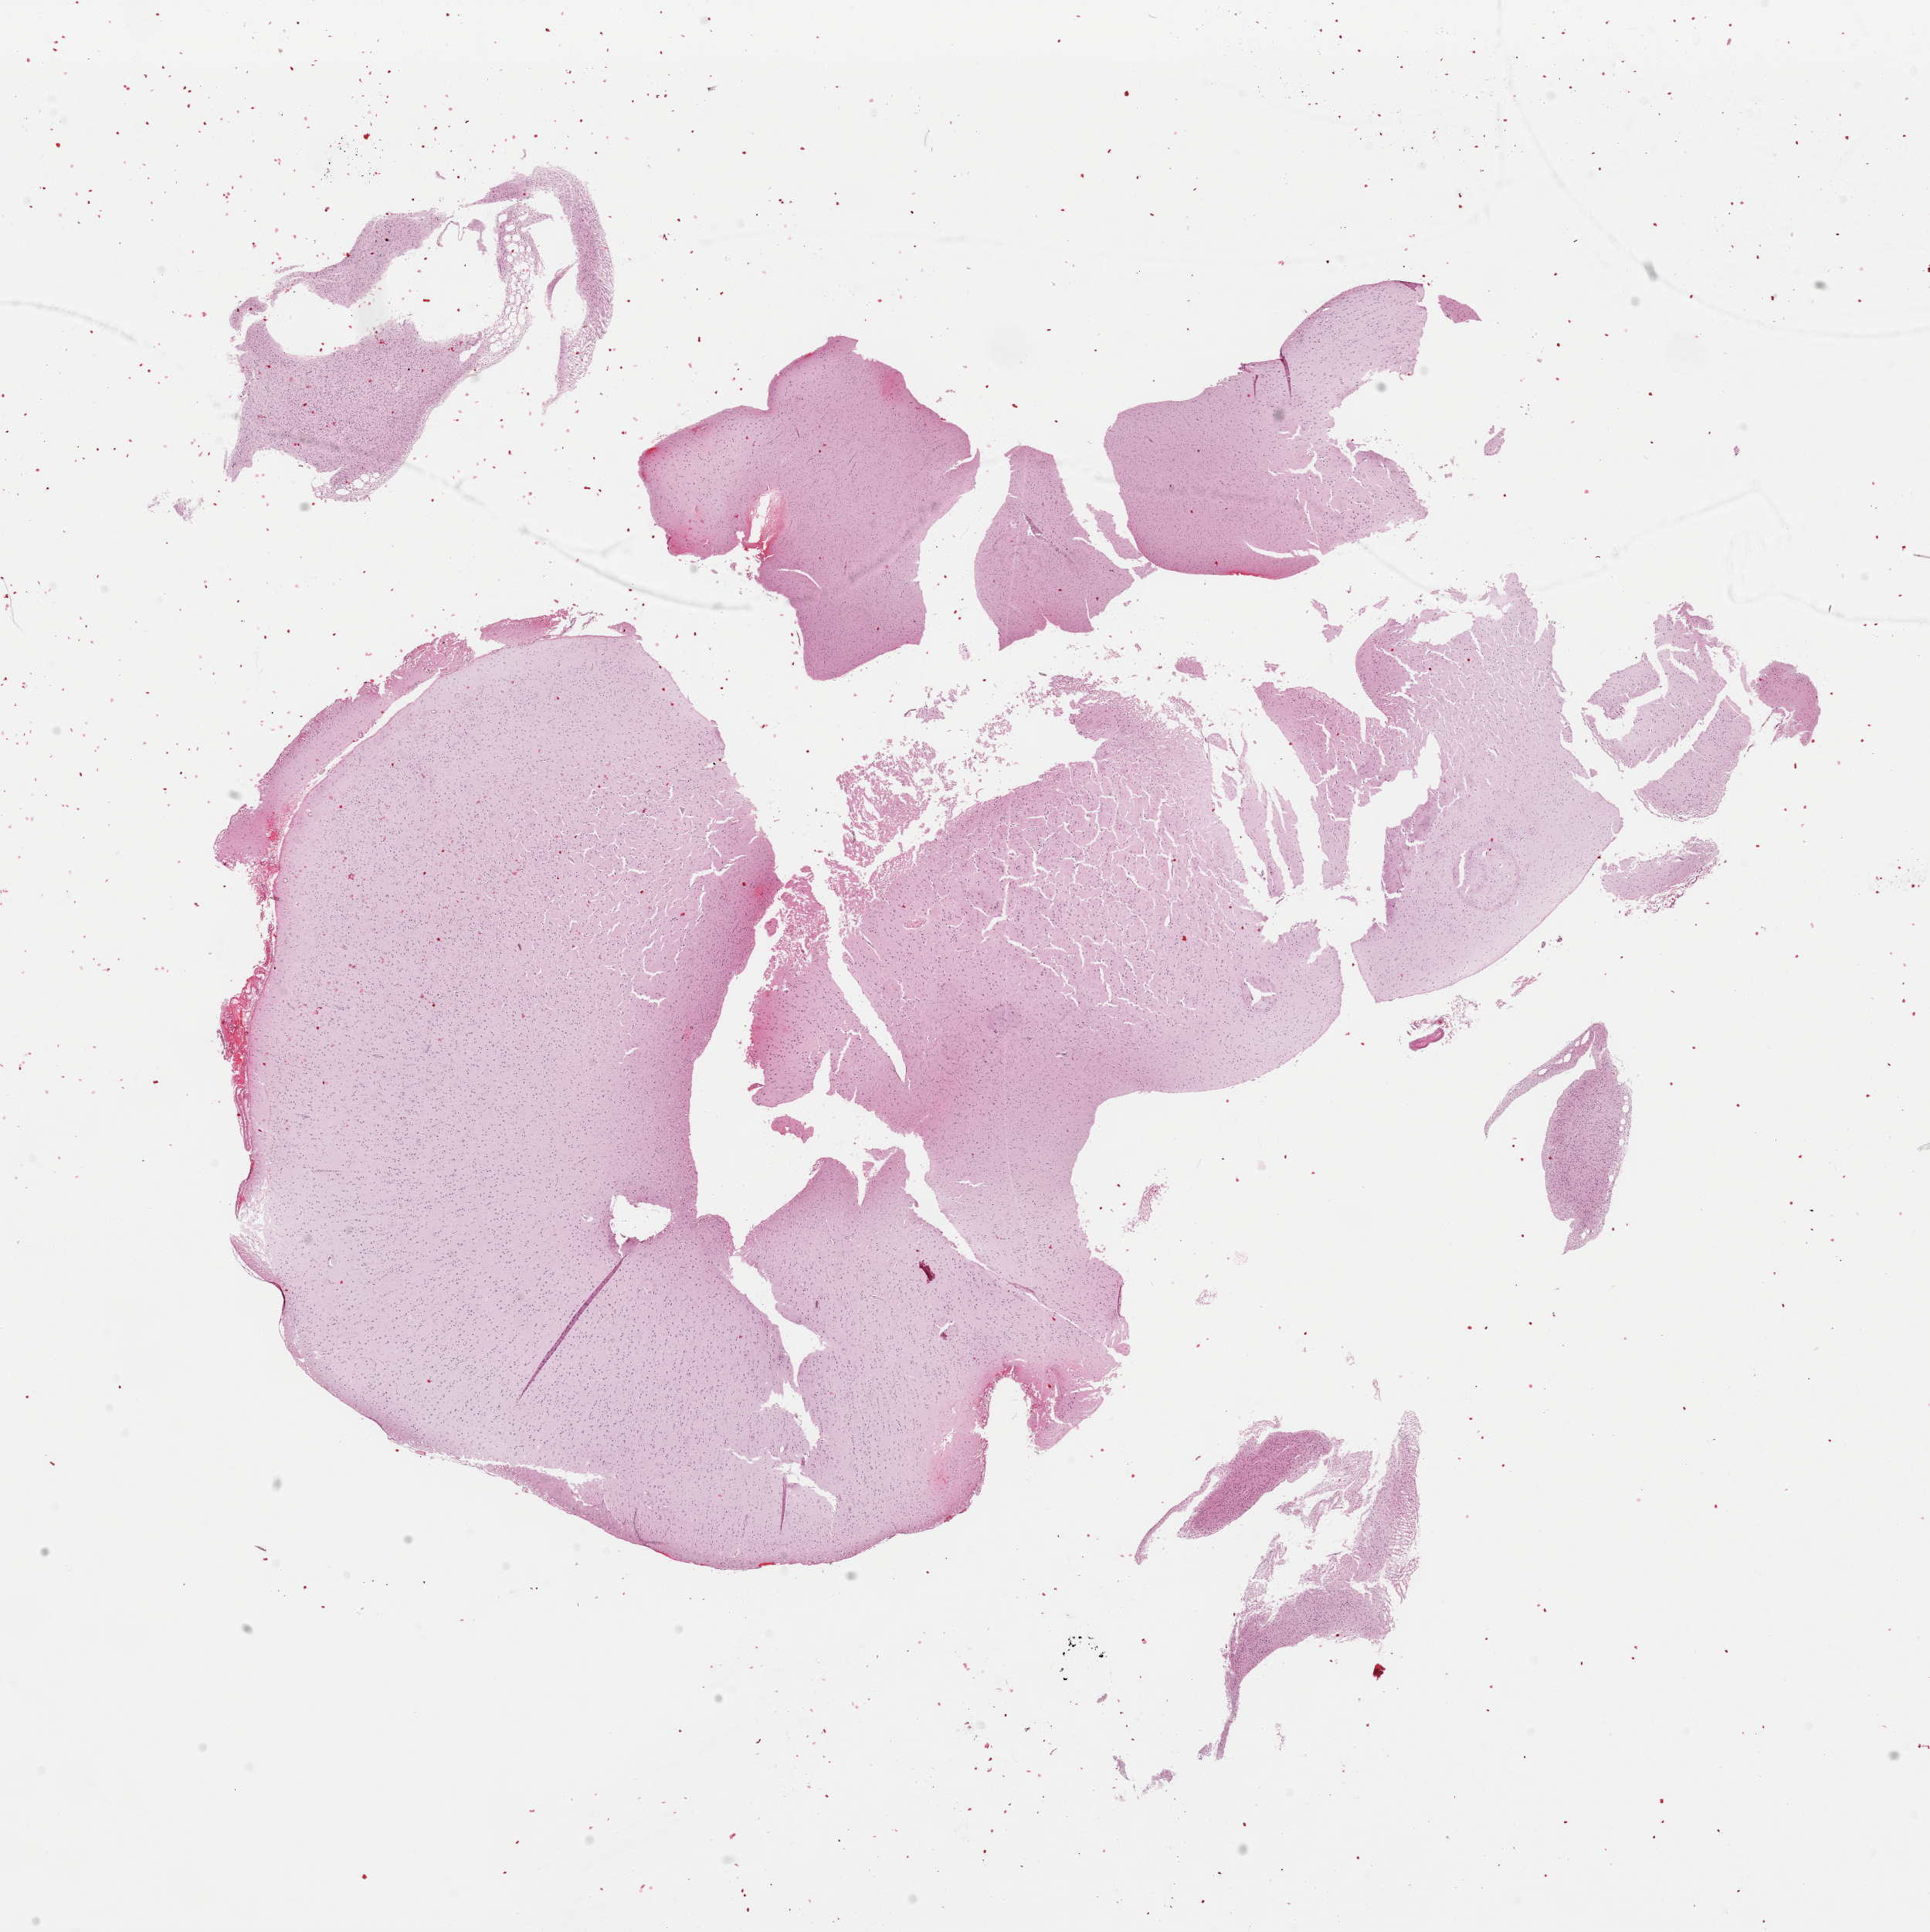
Whole-slide histology image, Hematoxylin and eosin (H&E) stained, low-resolution overview of the scanned area, about 19.7 x 19.8 mm, FFPE section, primary tumour sample from the brain. Female patient; age at initial diagnosis 42 years. Histologic grade: G2 (moderately differentiated).
Pathologic diagnosis: Astrocytoma, NOS (cerebrum).